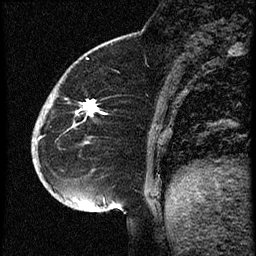
Breast MRI (dynamic contrast-enhanced), one sagittal slice. Position 16 of 60 along the scan axis. Dynamic contrast-enhanced study with each time point stored as its own series, time point 2 of 3 at this slice position (early post-contrast, ordered by acquisition time). 1.5 T. TE 4.2 ms, TR 18.9 ms. 2 mm slice thickness. 256 × 256 image matrix. Female patient. Case-level facts recorded for this patient, not image findings: setting: breast cancer imaged before/during neoadjuvant chemotherapy; receptor status: HR-positive, HER2-negative.
Annotated regions visible in this slice (semi-automatic segmentation, software-assisted and operator-edited):
- analysis volume of interest (the breast-tissue region the enhancement analysis was run in; not a lesion): box from (x=32, y=87) to (x=109, y=173) px
- tumour enhancement mask (voxels above the 100 % enhancement threshold inside the analysis volume of interest): (x=87, y=102)–(x=99, y=114)